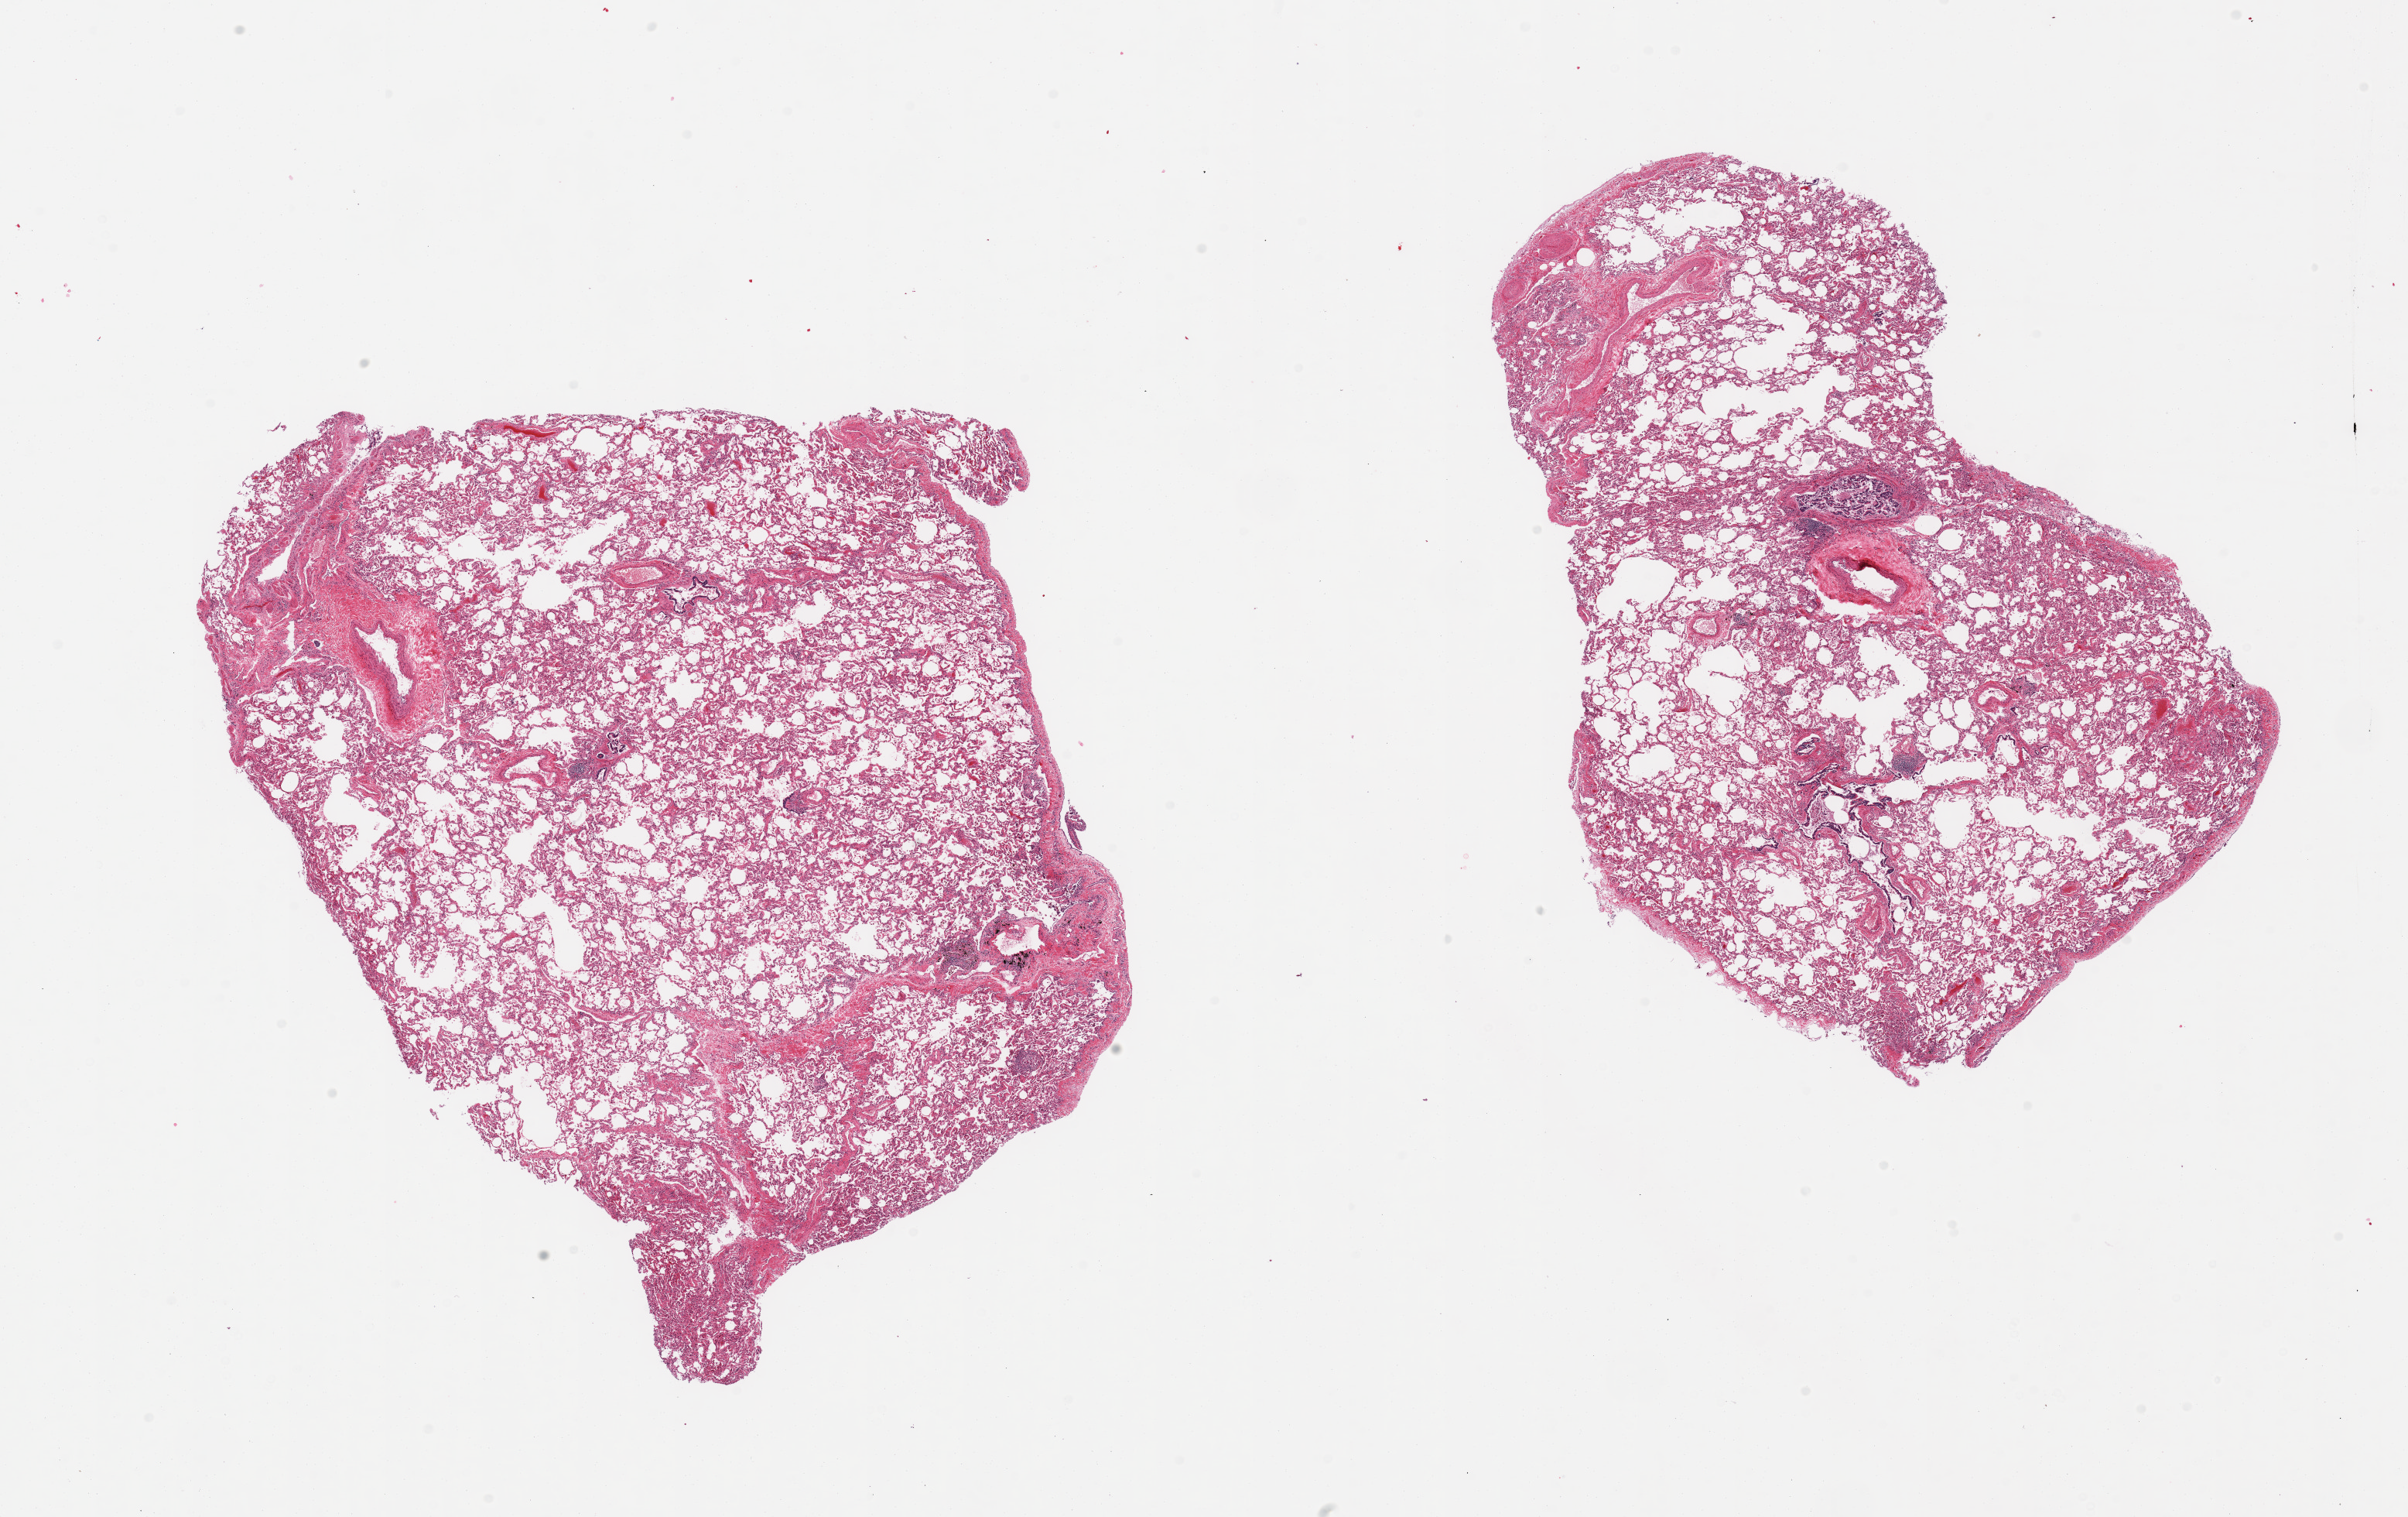
Whole-slide image, H&E stain, brightfield — whole scanned area (about 24.6 x 15.5 mm, from a 20x scan) shown as a low-resolution overview, PAXgene-fixed paraffin-embedded (PFPE) section, target tissue: lung, tissue donor sample. Donor sex: male.
Reviewer comment on this tissue sample: 2 pieces, trace congestion.